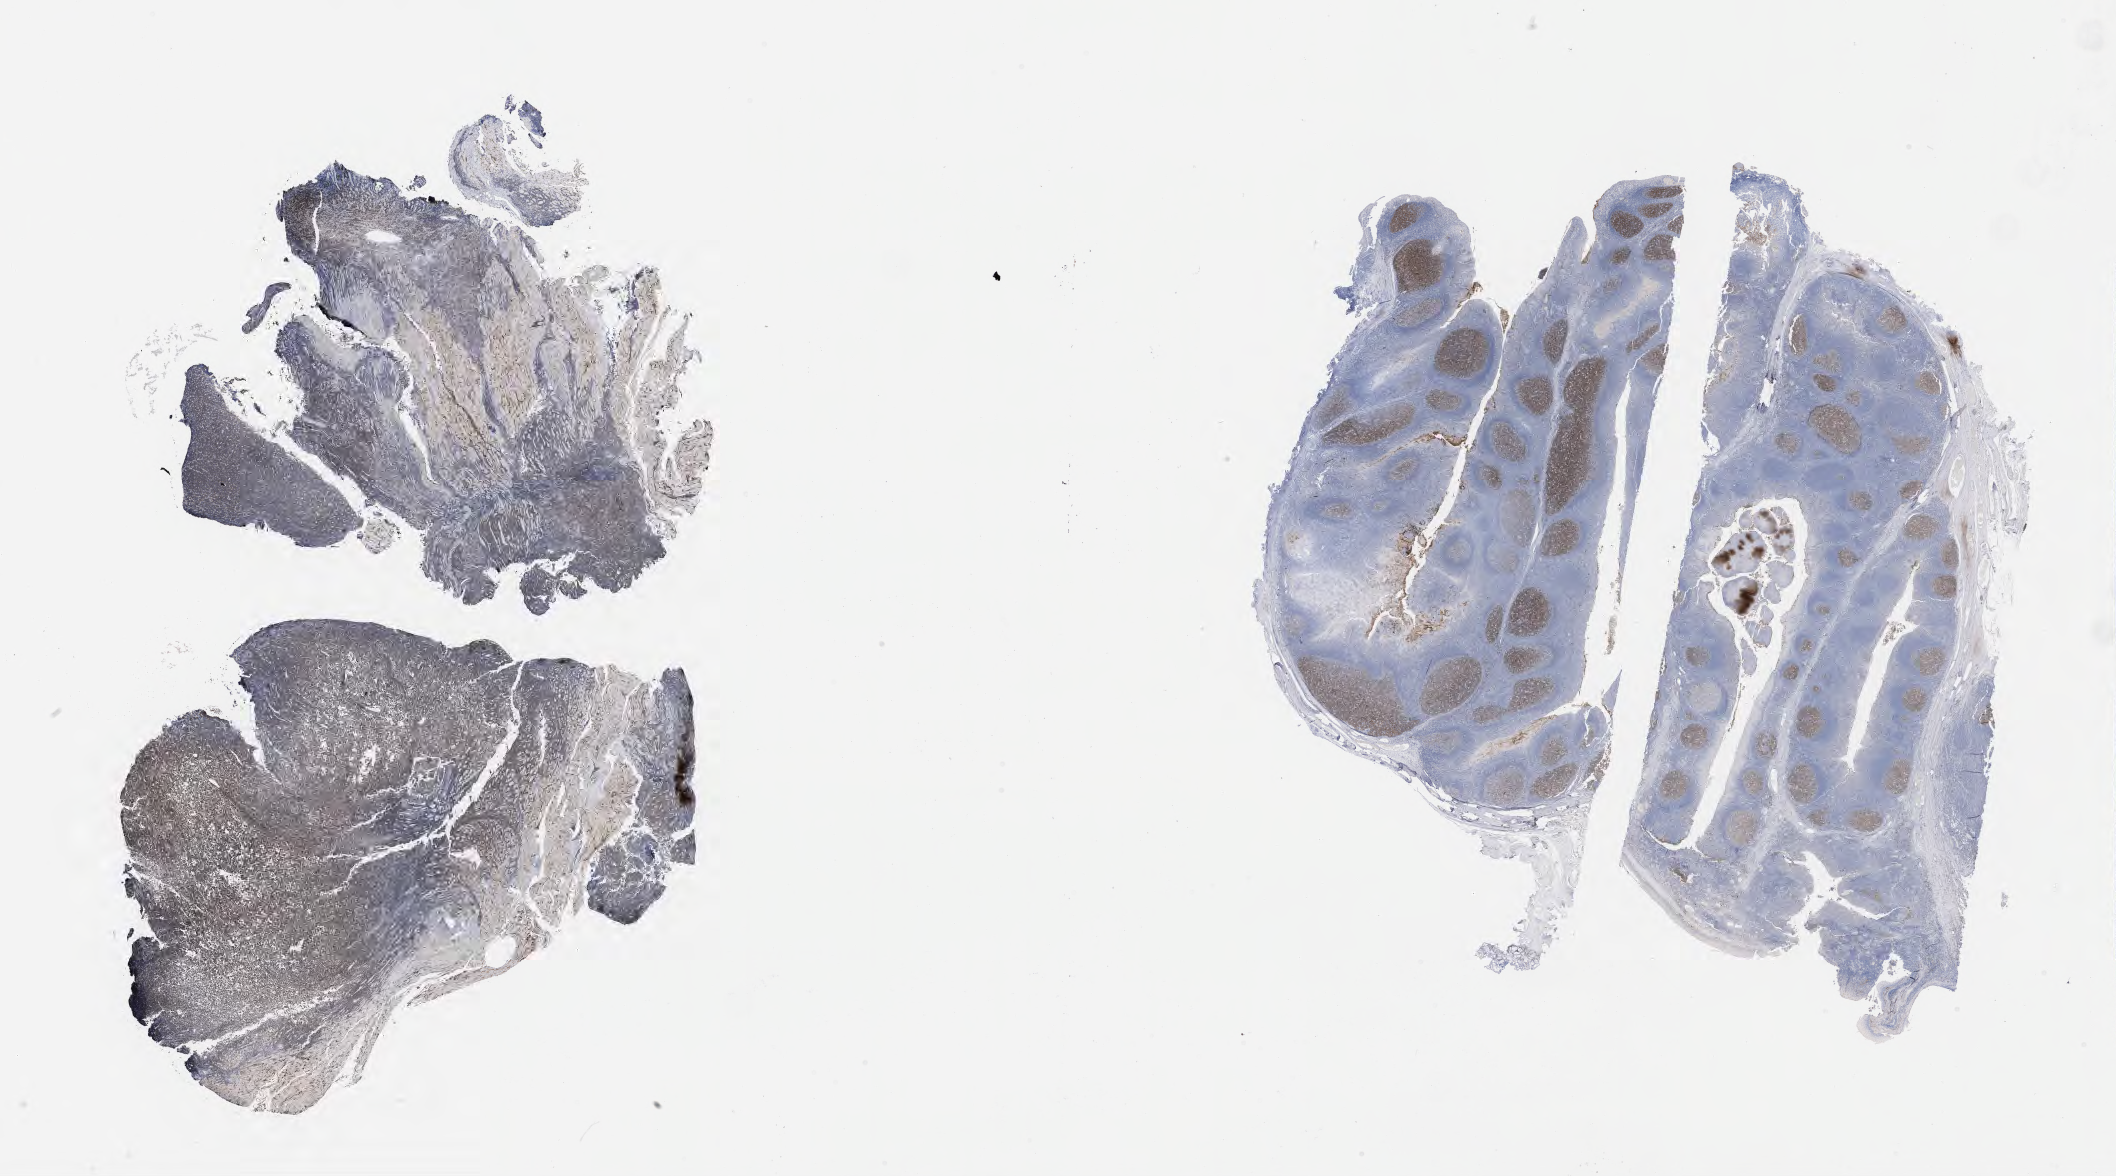
Immunohistochemistry (IHC) whole-slide image stained for CD10 — a low-resolution overview of the entire scanned area, about 34.2 x 19.0 mm. Specimen: tumor tissue. Male patient, aged 40.
Histologic diagnosis: Burkitt lymphoma, NOS.